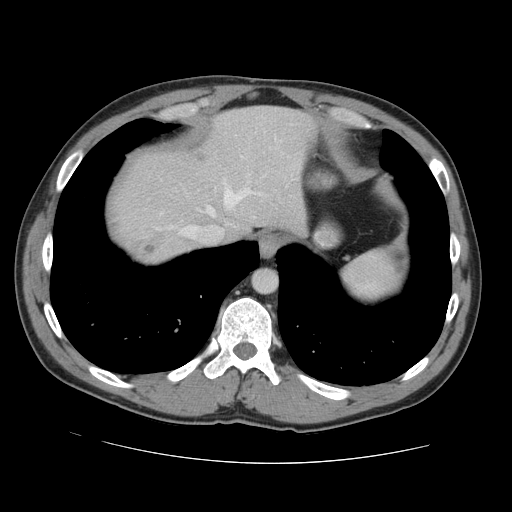
Contrast-enhanced abdominal CT, one axial slice; position 120 of 131 along the scan axis; 120 kVp; intravenous contrast given; soft-tissue window (W 400 / L 40 HU); 512 × 512 image matrix. Male patient, age 40 years. Case-level facts recorded for this patient, not image findings: diagnosis: colorectal cancer liver metastases, imaged before liver resection; multiple liver metastases: yes; largest metastasis: 2.9 cm; chemotherapy before resection: yes.
Outlined on this slice (expert manual segmentation):
- hepatic veins: bounding box [x1, y1, x2, y2] px = [183, 181, 262, 237]
- liver: [114, 107, 310, 263]
- planned liver remnant (the part of the liver to remain after resection): [129, 107, 311, 238]
- liver metastasis: [197, 154, 204, 160]
- liver metastasis: [146, 246, 156, 254]